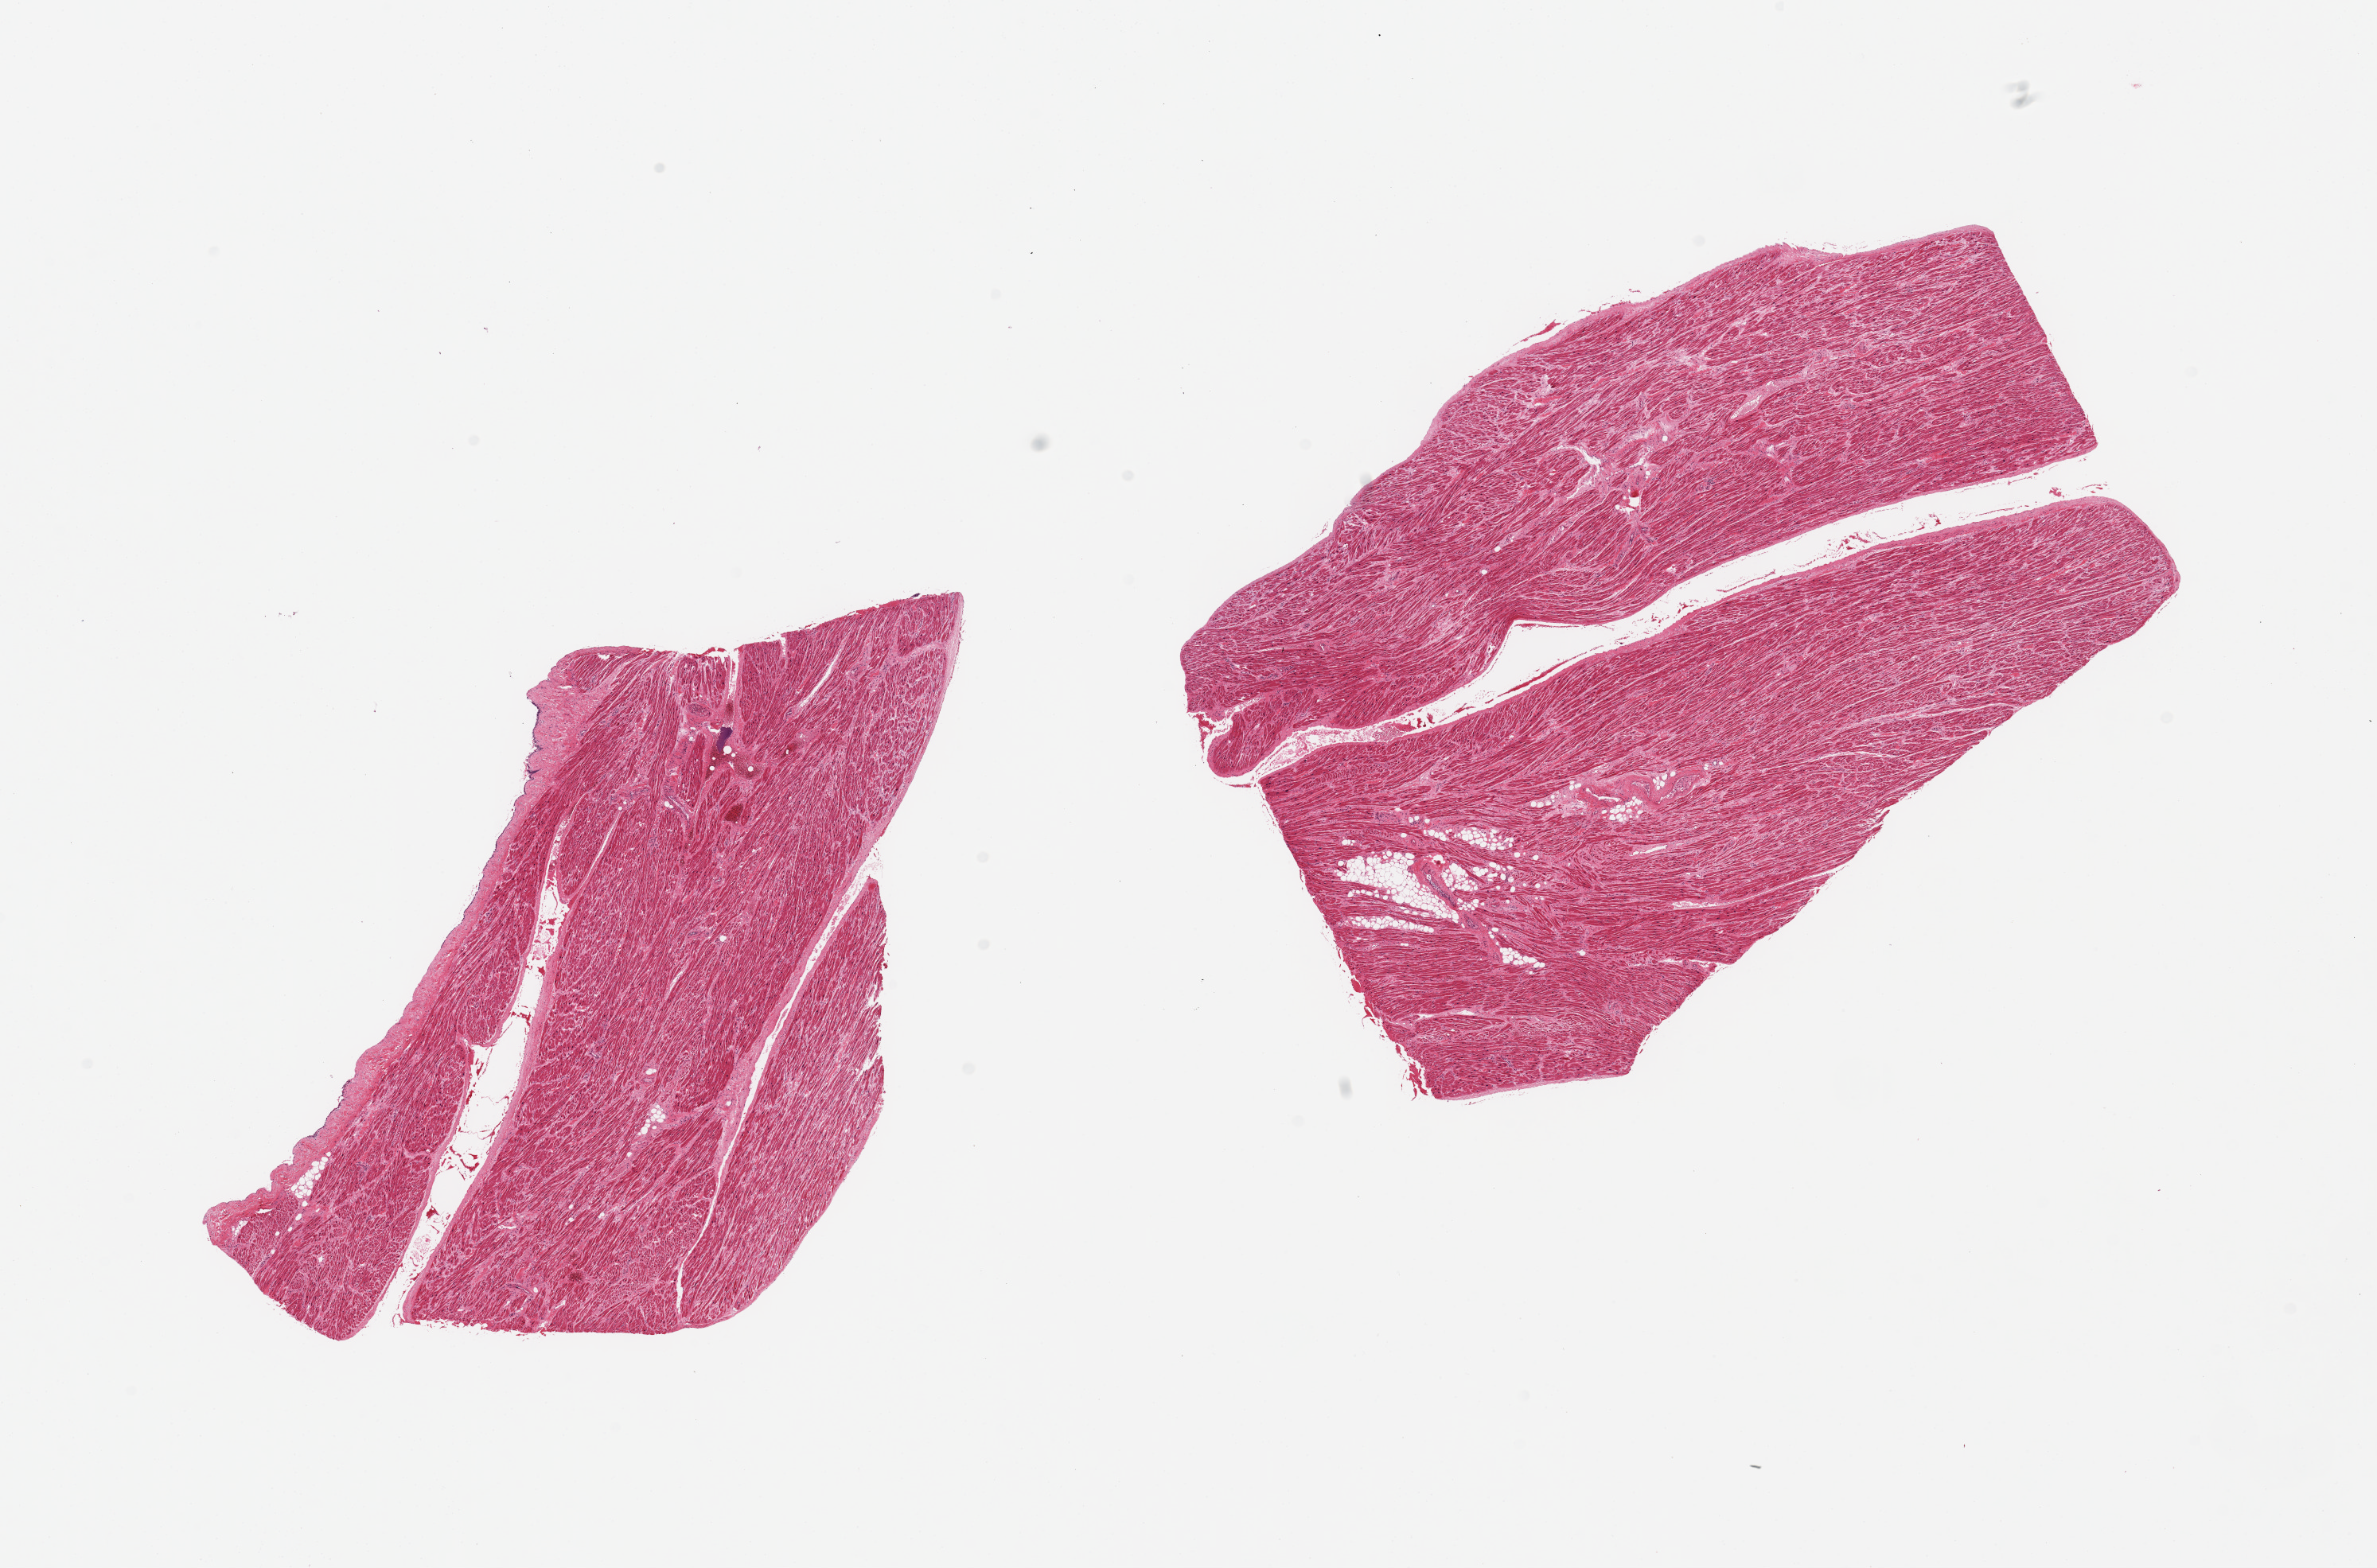
Whole-slide image, H&E stain, a low-resolution overview of the entire scanned area, about 23.6 x 15.6 mm (slide scanned at 20x); PAXgene-fixed, paraffin-embedded tissue; sampled site (target tissue): auricular appendage; tissue donor sample. Donor sex: female.
Pathologist's review note for this sample: 2 pieces; 5% internal fat.